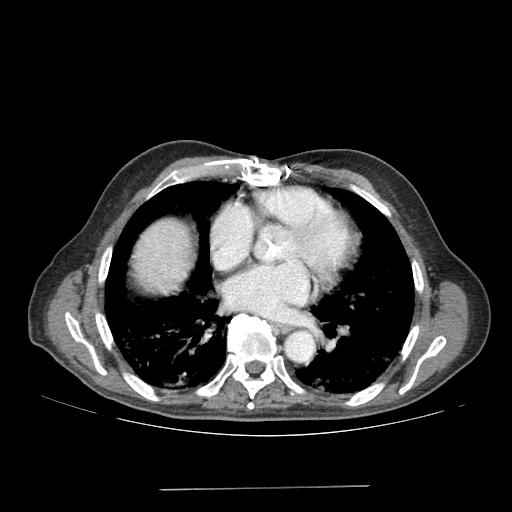
Contrast-enhanced abdominal CT (liver protocol), one axial slice; position 178 of 192 along the scan axis; reconstruction kernel SOFT; 120 kVp; soft-tissue window (W 400 / L 40 HU); 2.5 mm slice thickness; 512 × 512 image matrix, field of view 400 × 400 mm. Case-level facts recorded for this patient, not image findings: diagnosis: hepatocellular carcinoma (patient treated with transarterial chemoembolisation; whether this scan precedes or follows treatment is not stated here); TNM stage (as recorded): Stage-IVA; Child-Pugh class: A; tumour differentiation: poorly differentiated; tumour nodularity: uninodular.
Outlined on this slice (semi-automatically segmented with operator editing):
- liver parenchyma outside the tumour (the mass and vessels are separate outlines, so this box may not span the whole liver): box from (x=134, y=220) to (x=190, y=292) px